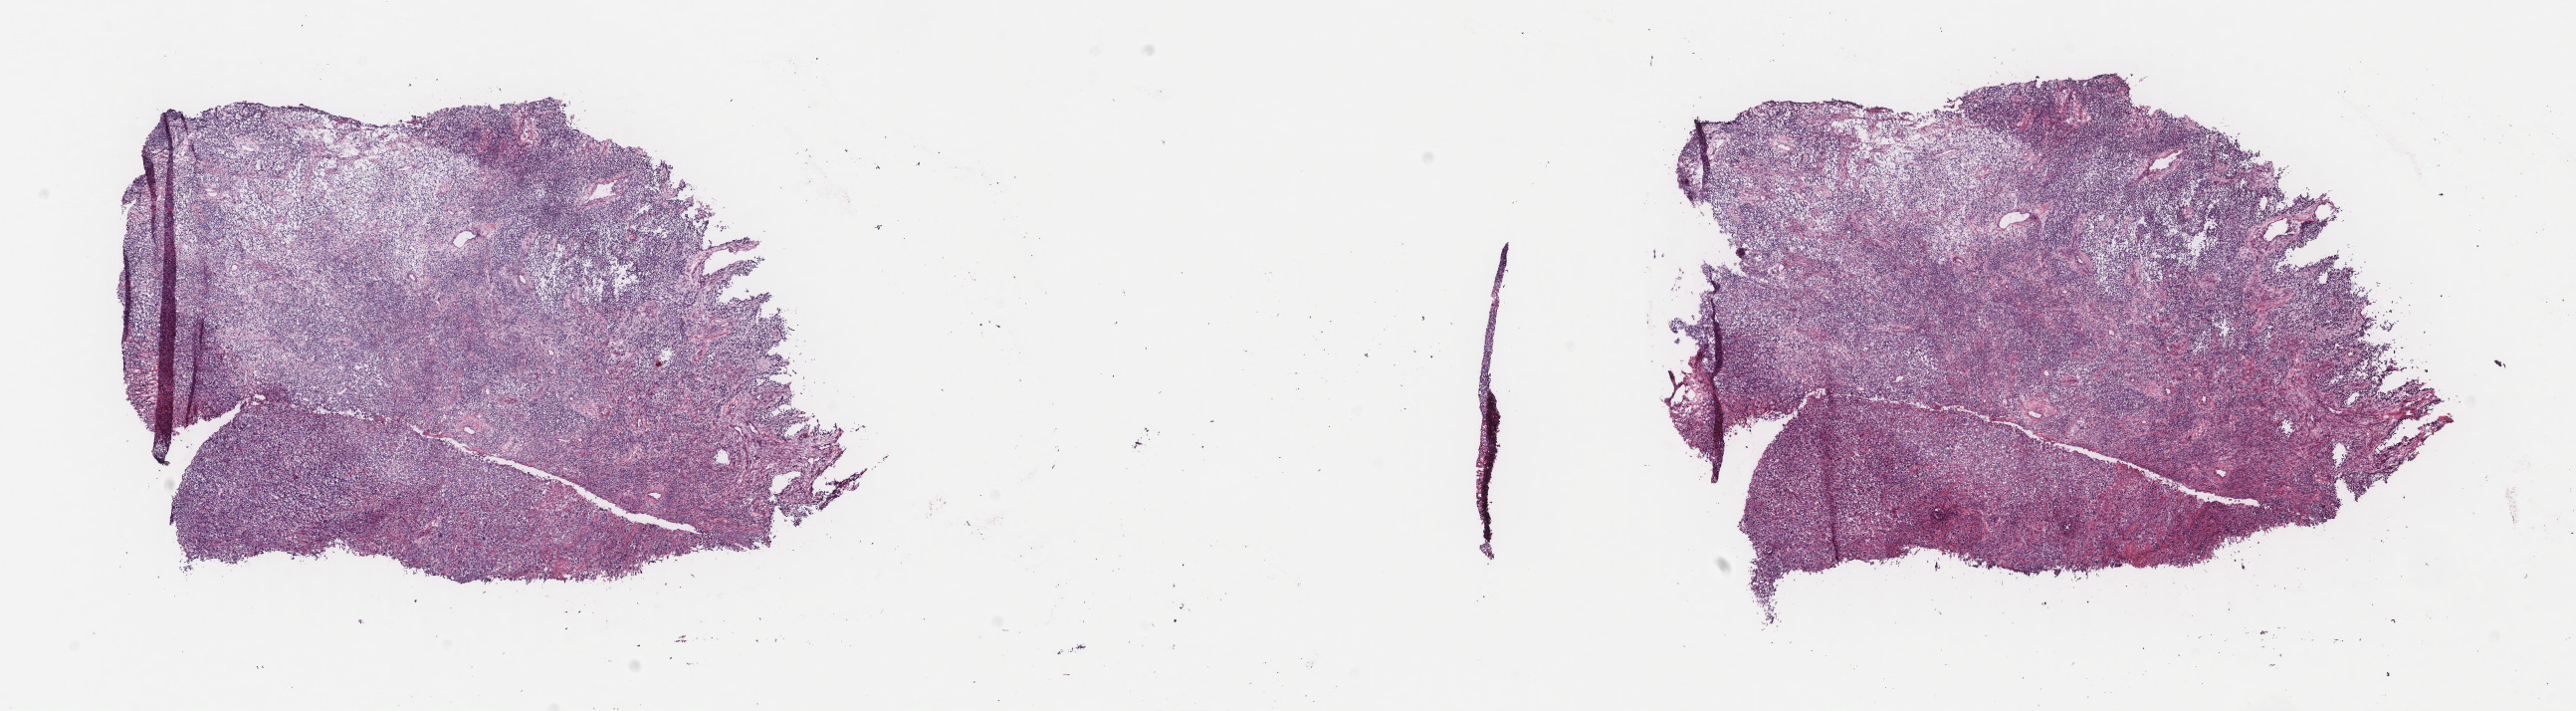
Hematoxylin and eosin (H&E) stained whole-slide image, a low-resolution overview of the entire scanned area, about 20.5 x 5.7 mm; frozen section from the top of the tissue portion; metastatic tumour sample, sampled site not recorded. Patient: male, age at initial diagnosis 73 years. Pathologist review of this section (percent, as recorded): tumour cells 100%, tumour nuclei 85%, normal cells 0%, stromal cells 0%, necrosis 0%. Inflammatory infiltration, as recorded: lymphocyte infiltration 0%, monocyte infiltration 0%, neutrophil infiltration 0%.
- this section: metastatic tumour tissue
- patient diagnosis: Malignant melanoma, NOS